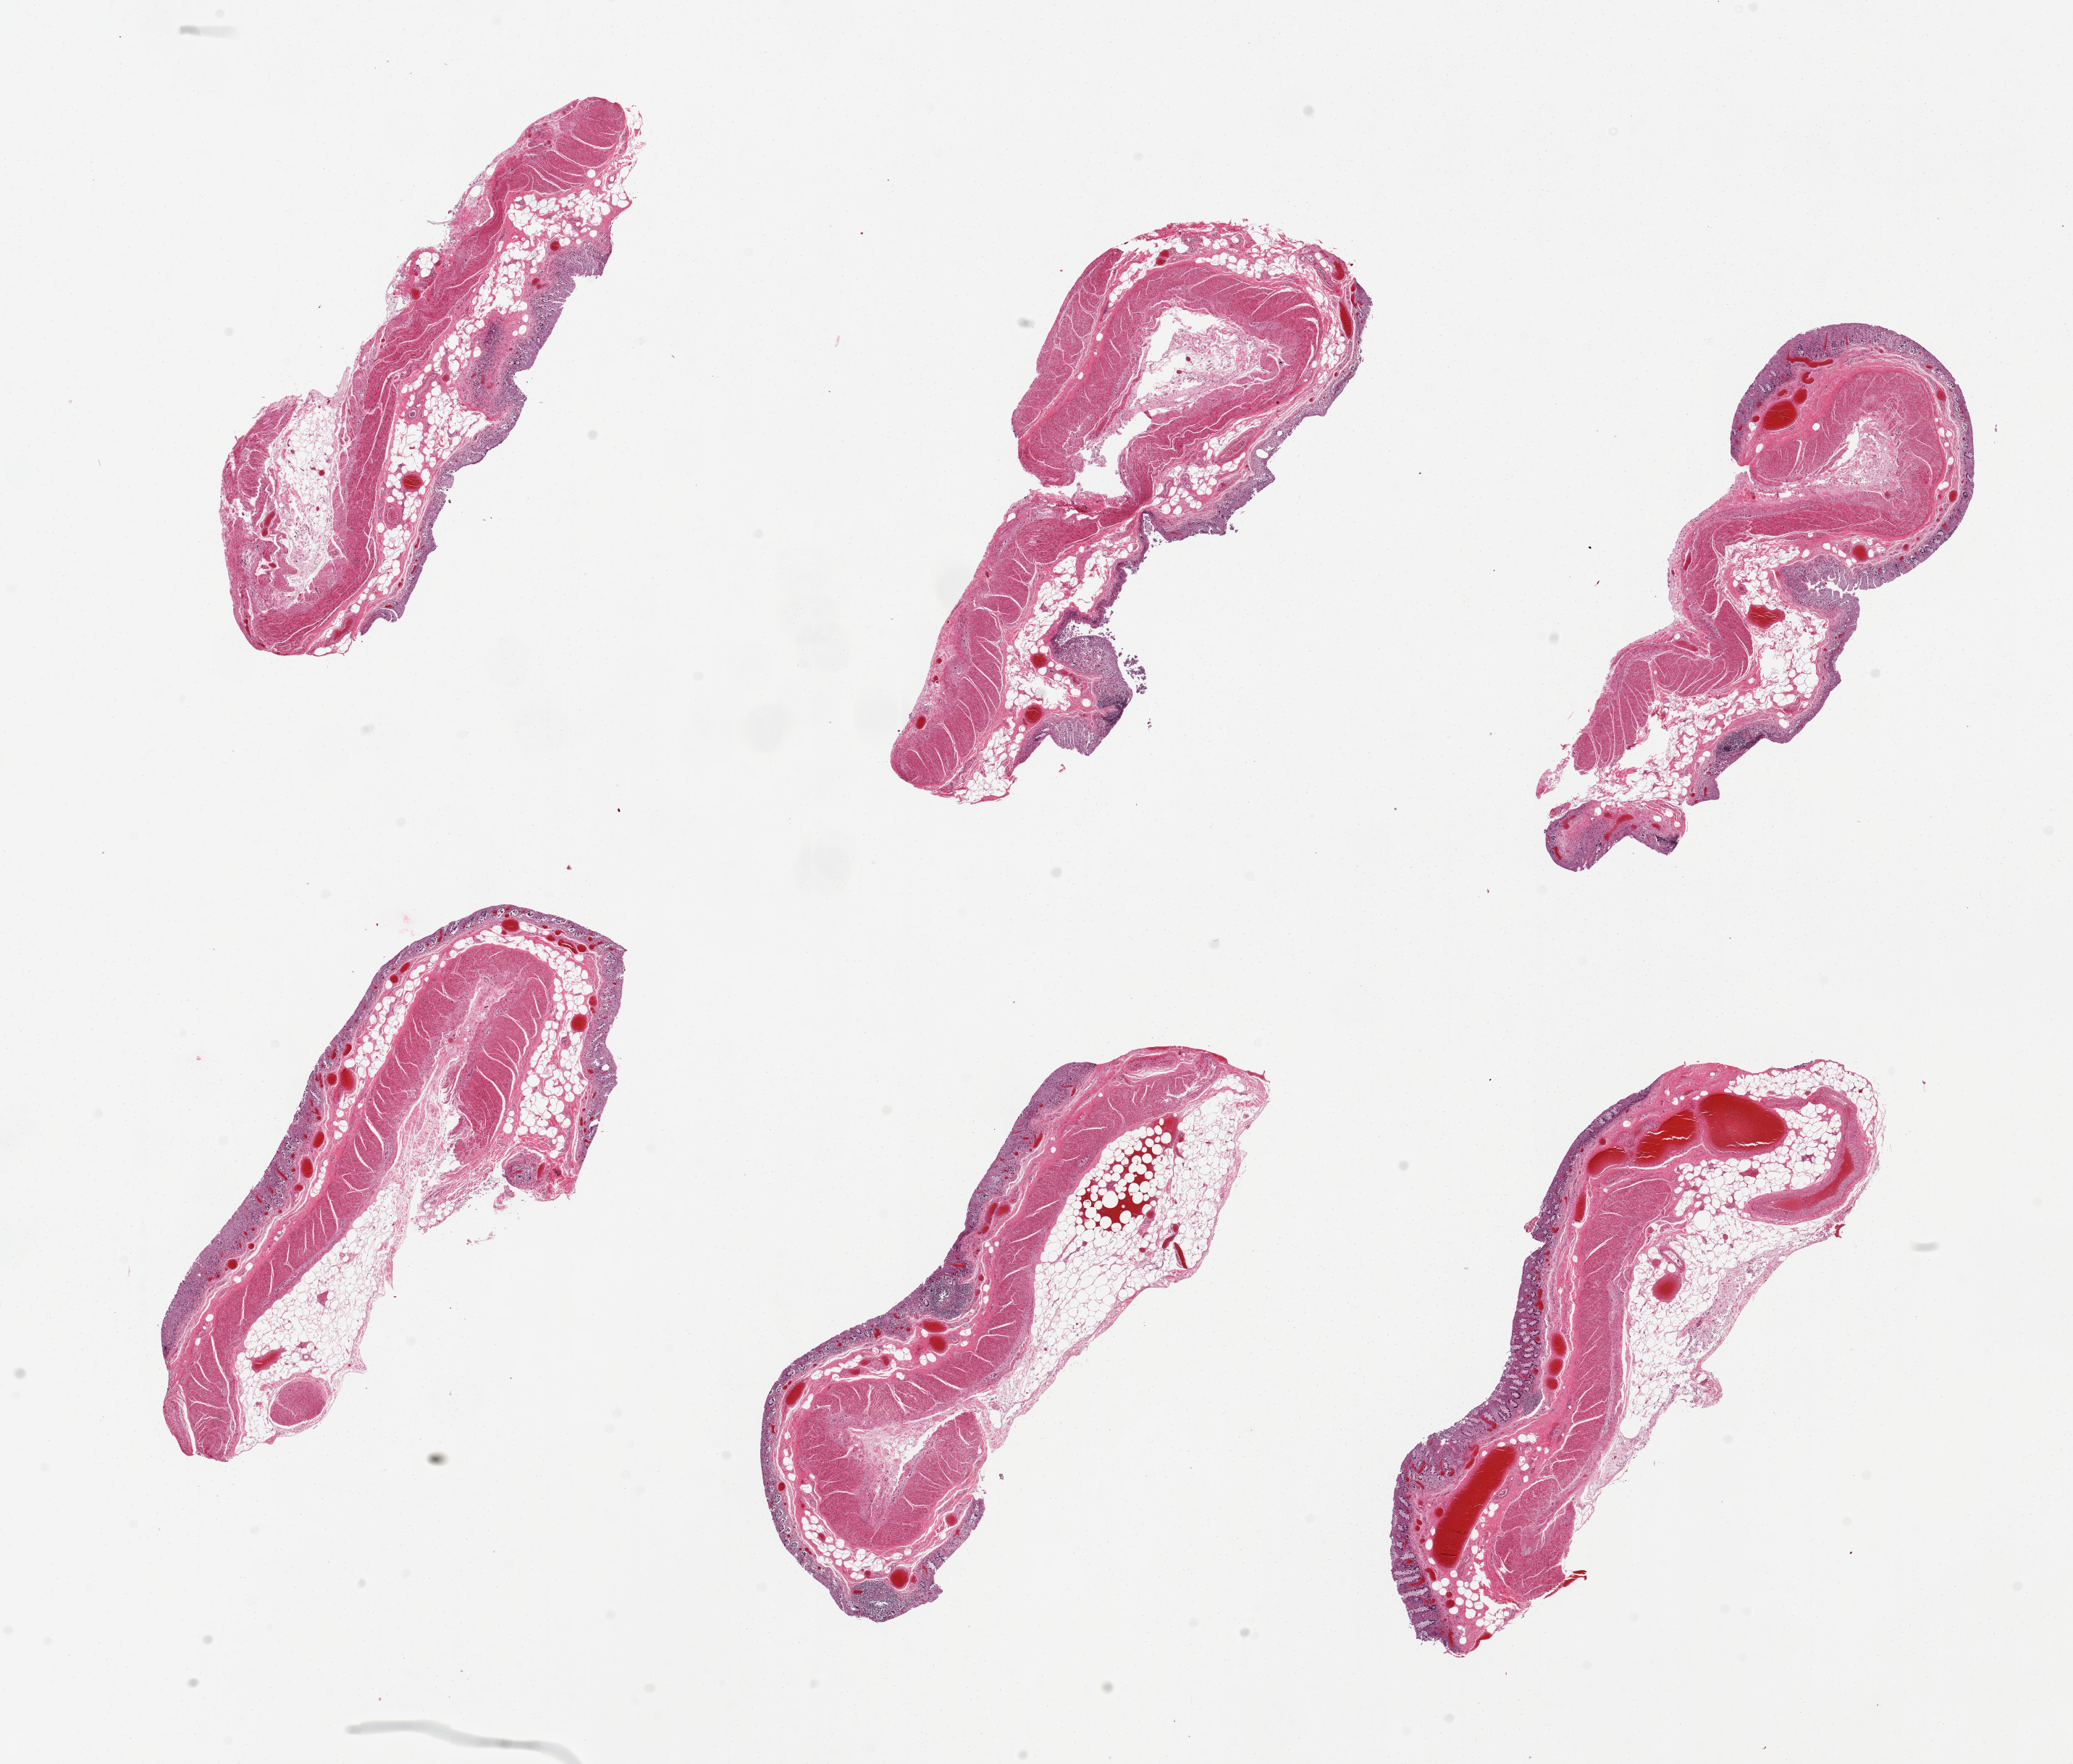
H&E whole-slide image, a low-resolution overview of the entire scanned area, about 22.6 x 19.3 mm. PAXgene-fixed paraffin-embedded (PFPE) section. Target tissue: transverse colon. Tissue donor sample. Donor: male.
* reviewer comment on this tissue sample: 6 pieces, mucosa badly autolyzed/sloughed